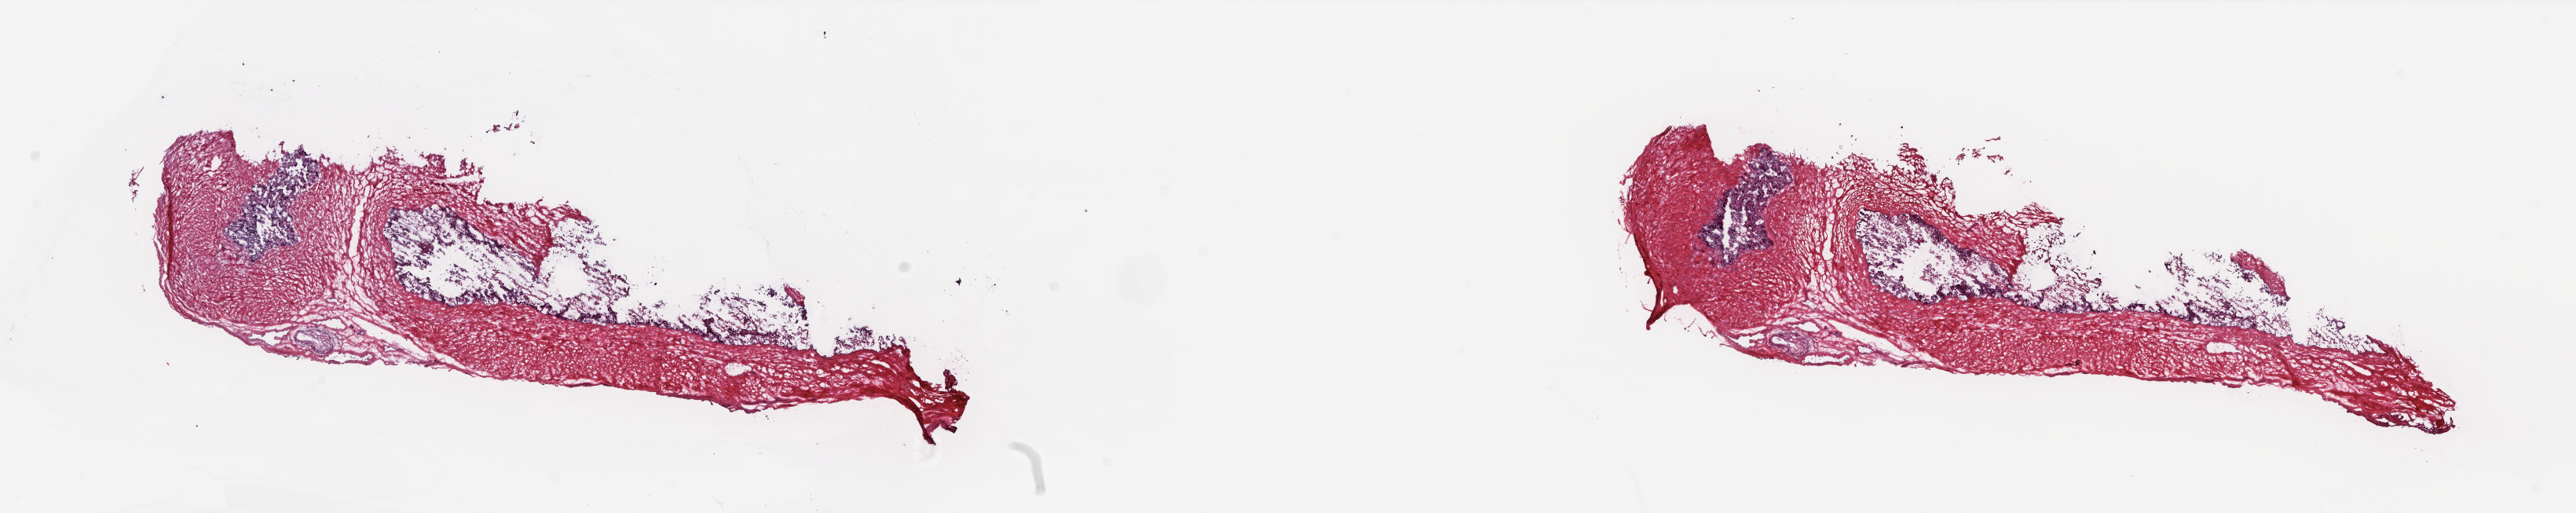
Hematoxylin and eosin (H&E) stained whole-slide image — low-resolution overview of the scanned area, about 26.5 x 5.3 mm (slide scanned at 20x). Frozen section from the top of the tissue portion. Solid tissue normal (non-tumour tissue) sample from the prostate. Patient: male, age at initial diagnosis 59 years. Slide review estimates, as recorded: tumour cells 0%, tumour nuclei 0%, normal cells 40%, stromal cells 60%, necrosis 0%. Infiltration values recorded for this section: lymphocyte infiltration 40%, monocyte infiltration 20%, neutrophil infiltration 20%.
• this section: solid tissue normal sample (biorepository sample class)
• patient diagnosis: Adenocarcinoma, NOS